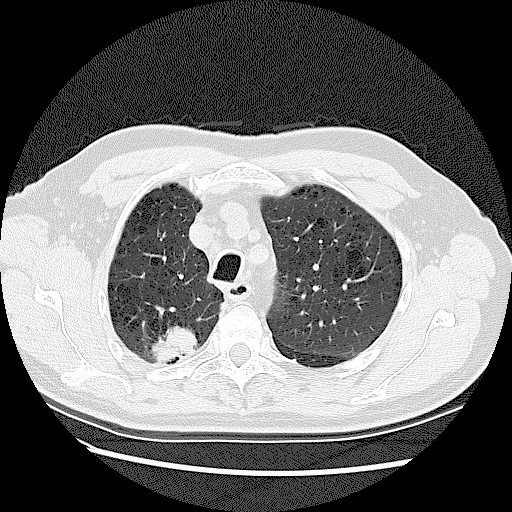
Chest CT (low-dose screening protocol), one axial image; first (baseline) screen; lung window (W 1500 / L -600 HU); 2.5 mm slice thickness; lung (sharp) reconstruction kernel (LUNG); 120 kVp. Male participant, aged 72 years at enrolment.
Lesion marked by an expert reader, bounding box (x1, y1, x2, y2) in pixels: (136, 308, 213, 375). The screening reader recorded 2 non-calcified nodules or masses ≥4 mm on this exam; which of them this box marks is not recorded. Lung cancer was diagnosed 42 days after this screen: adenocarcinoma, NOS, right upper lobe, stage IV (AJCC 6th edition), 45 mm at pathology.